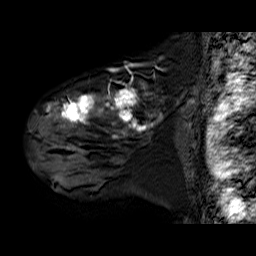
Breast MRI (dynamic contrast-enhanced), one sagittal slice. Position 47 of 60 along the scan axis. Dynamic contrast-enhanced series, time point 2 of 6 at this slice position (early post-contrast). 1.5 T. TE 6.3 ms, TR 32.9 ms. 4 mm slice thickness. 256 × 256 image matrix, field of view 200 × 200 mm. Female patient. Case-level facts recorded for this patient, not image findings: setting: breast cancer imaged before/during neoadjuvant chemotherapy; receptor status: HER2-positive.
Outlined on this slice (semi-automatically segmented with operator editing):
- analysis volume of interest (the breast-tissue region the enhancement analysis was run in; not a lesion): bounding box (x1, y1, x2, y2) in pixels: (30, 80, 182, 180)
- tumour enhancement mask (voxels above the 100 % enhancement threshold inside the analysis volume of interest): (47, 85, 158, 138)